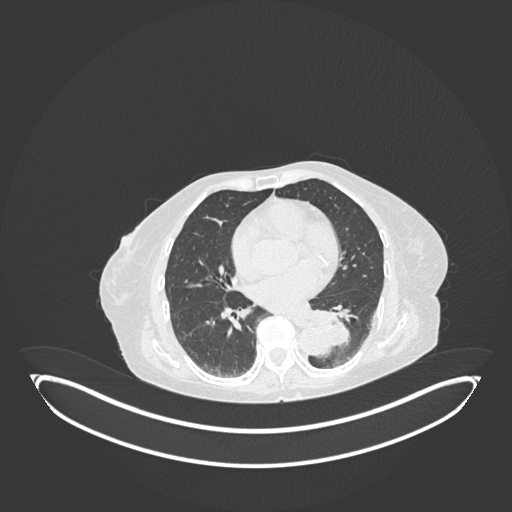
Chest CT, one axial slice. Slice 50 of 189 in the series (ordered by position). Reconstruction kernel B30f. 120 kVp. Lung window (W 1500 / L -600 HU). 1 mm slice thickness. 512 × 512 image matrix. Patient: female, 82 years. From the clinical record (not read from this slice): clinical TNM (as recorded): T1b N0 M1.
Structures marked on this image (bounding box drawn by a radiologist):
- lung tumour (recorded histology: adenocarcinoma): bounding box (x1, y1, x2, y2) in pixels: (312, 306, 352, 353)